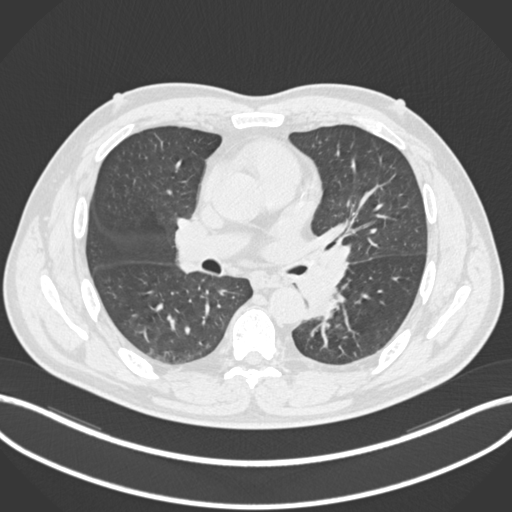
Chest CT, one axial slice. Slice 124 of 223 in the series (ordered by position). Reconstruction kernel B30f. 120 kVp. Lung window (W 1500 / L -600 HU). 1 mm slice thickness. 512 × 512 image matrix. Patient: male, 50 years. From the clinical record (not read from this slice): clinical TNM (as recorded): T2a N3 M0.
Annotated regions visible in this slice (rectangle marked by the reading radiologist):
- lung tumour (recorded histology: squamous cell carcinoma): bounding box [x1, y1, x2, y2] px = [292, 241, 353, 319]